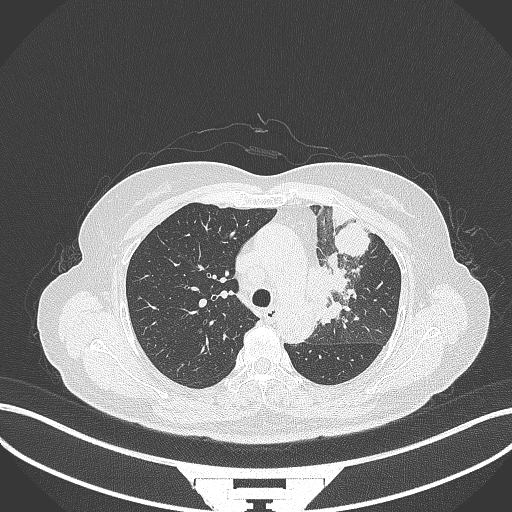
Chest CT, one axial slice. Slice 235 of 382 in the series (ordered by position). Reconstruction kernel B70f. Lung window (W 1500 / L -600 HU). 1 mm slice thickness. 512 × 512 image matrix, field of view 400 × 400 mm. Female patient, age 64 years. From the clinical record (not read from this slice): clinical TNM (as recorded): T2a N2 M0.
Structures marked on this image (bounding box drawn by a radiologist):
- lung tumour (recorded histology: adenocarcinoma): bounding box <308,250,356,326> (left, top, right, bottom; pixels)
- lung tumour (recorded histology: adenocarcinoma): <332,222,375,257>